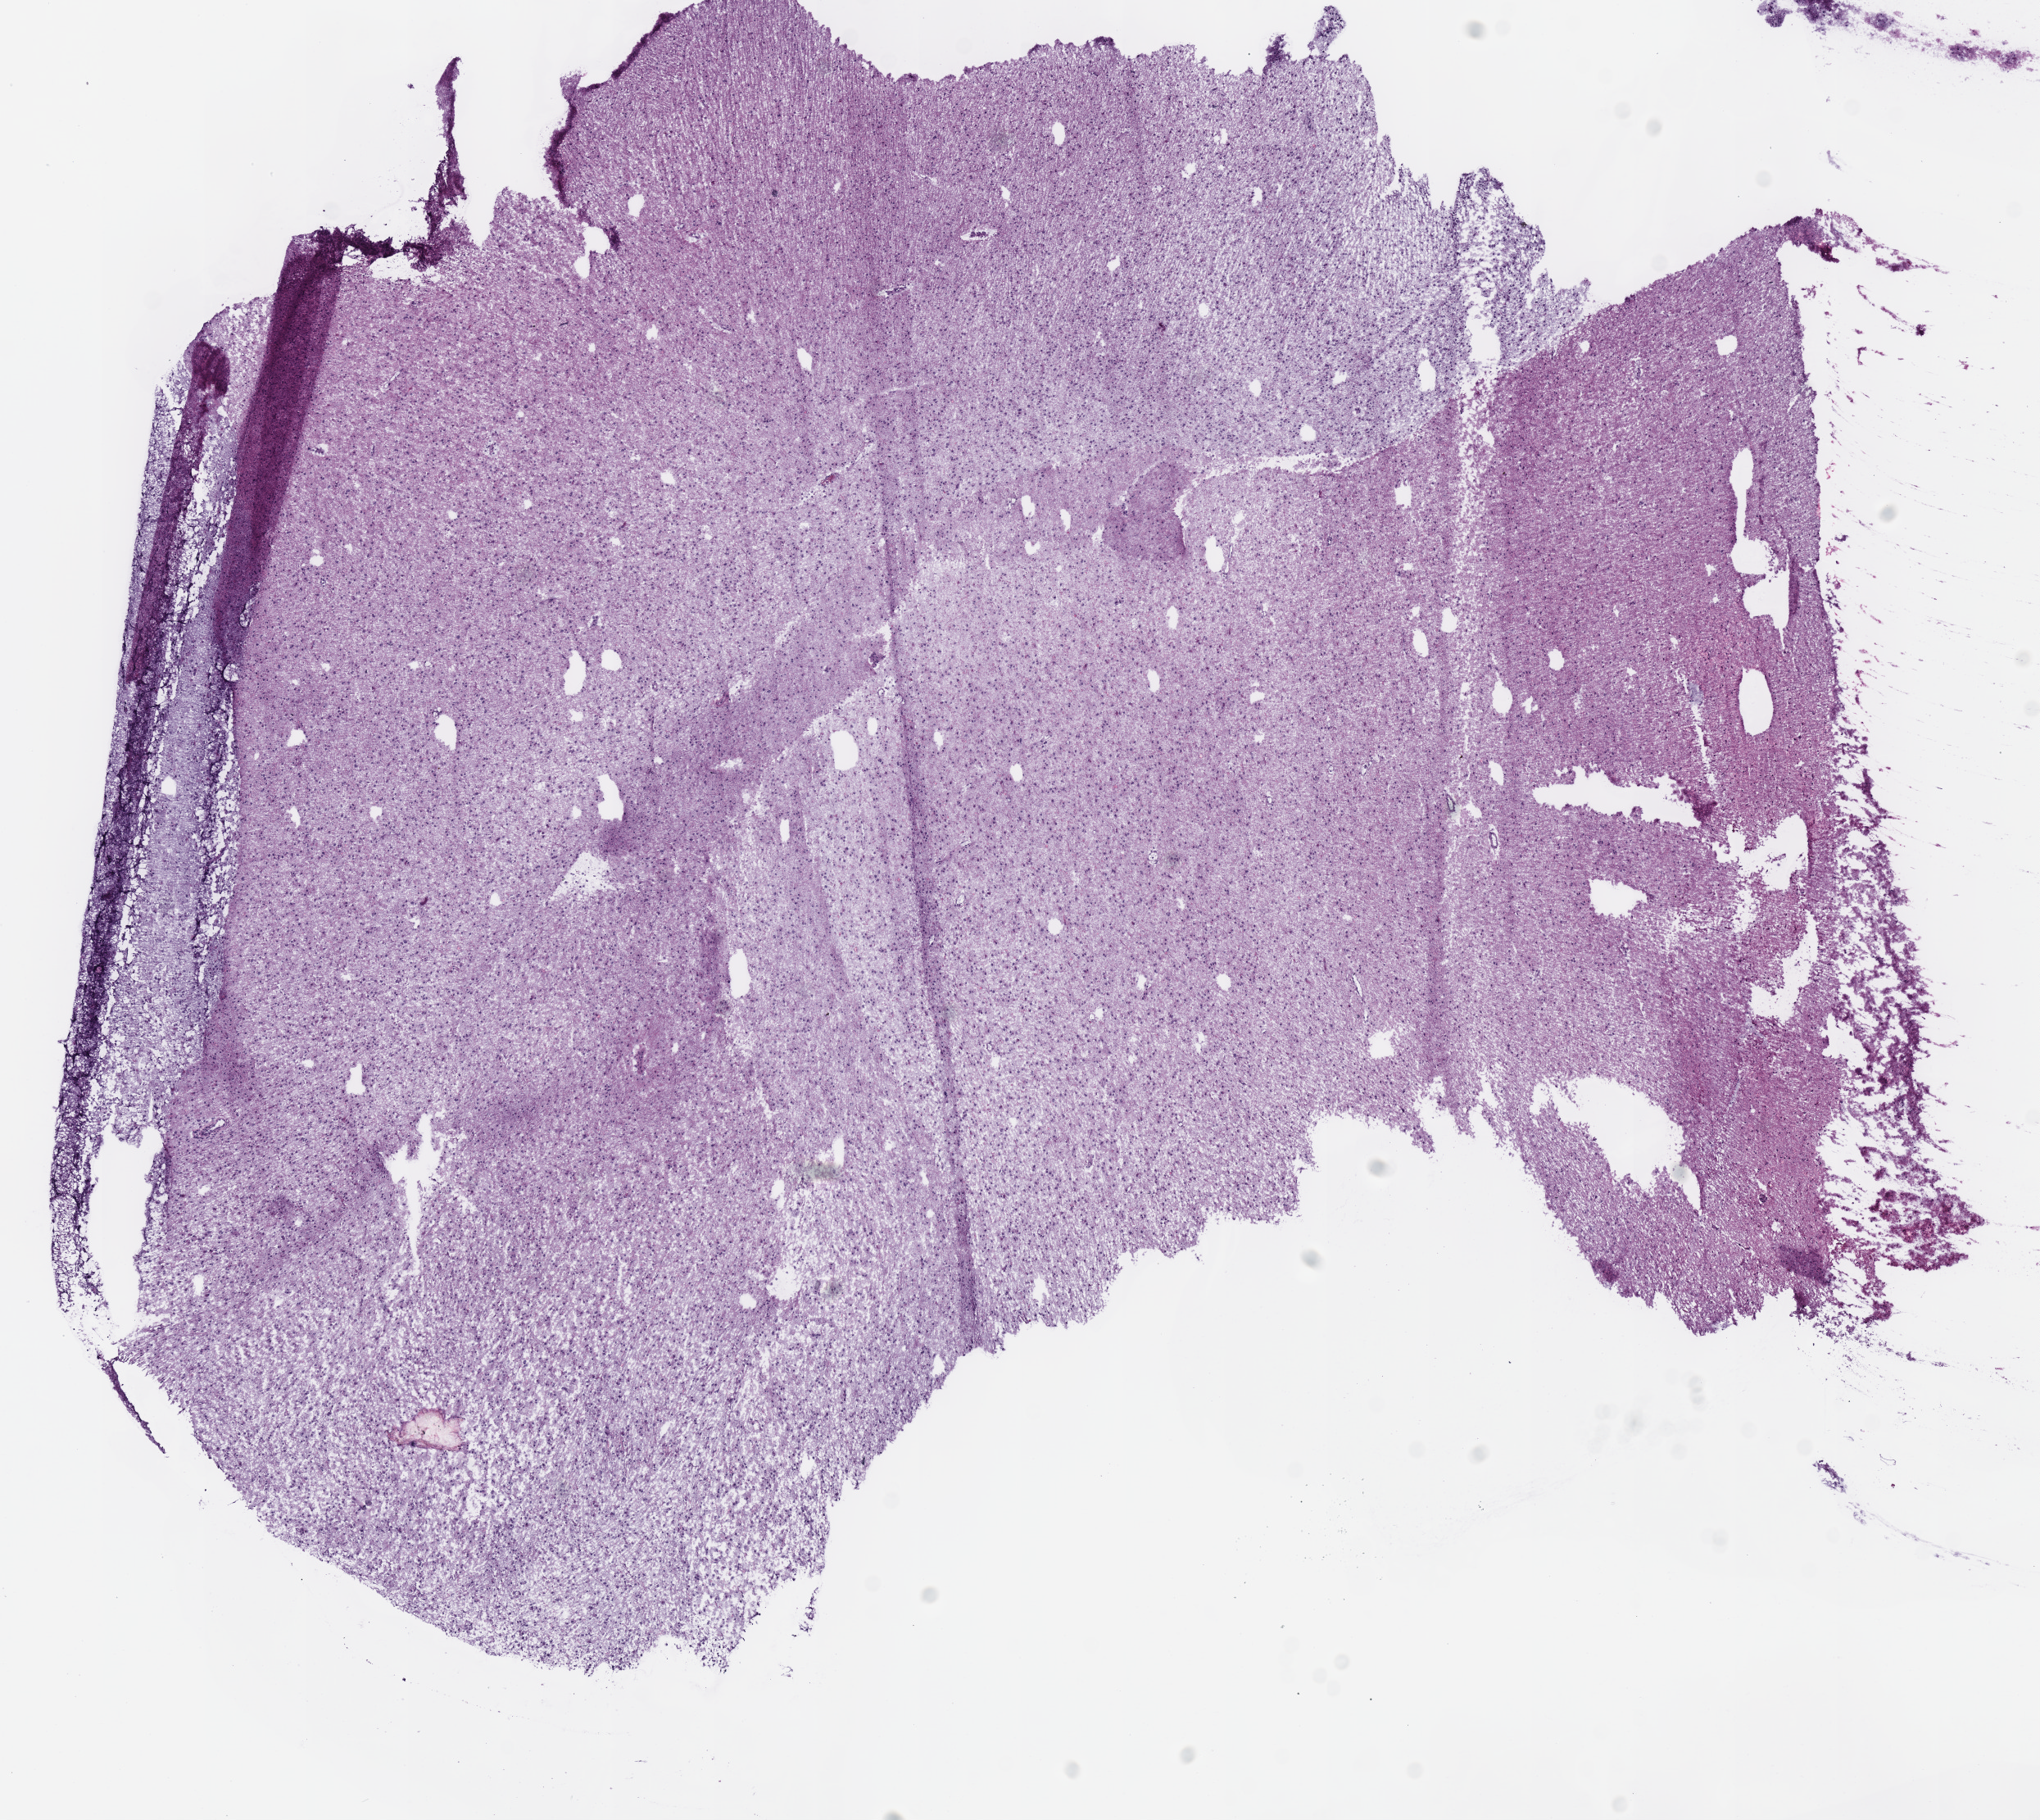
Digitized H&E-stained tissue section (whole slide) — a low-resolution overview of the entire scanned area, about 9.8 x 8.7 mm (slide scanned at 40x), frozen section, brain, primary tumour sample. Male, age 29 years at initial diagnosis. Composition of this section per pathologist review: tumour cells 100%, tumour nuclei 75%.
Histologic diagnosis: Mixed glioma (cerebrum).